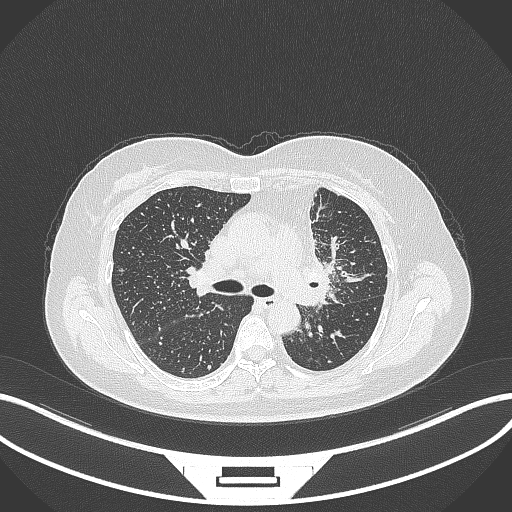
Chest CT, one axial slice. Position 209 of 348 along the scan axis. Reconstruction kernel B70f. Lung window (W 1500 / L -600 HU). 1 mm slice thickness. 512 × 512 image matrix, field of view 400 × 400 mm. Patient: female, 49 years. From the clinical record (not read from this slice): clinical TNM (as recorded): T1c N0 M1.
Structures marked on this image (rectangle marked by the reading radiologist):
- lung tumour (recorded histology: adenocarcinoma): box from (x=294, y=252) to (x=337, y=311) px